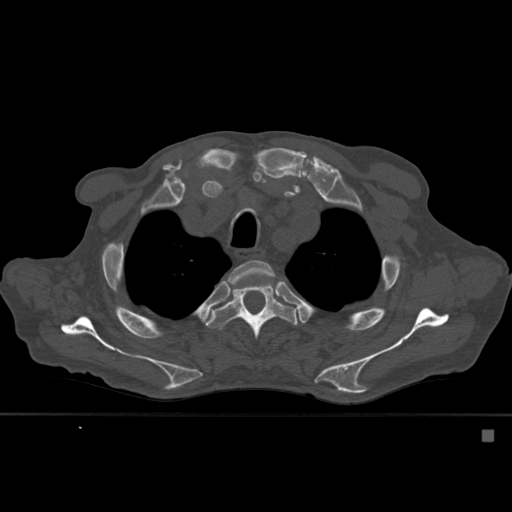
CT including the spine, one axial slice. Slice 421 of 527 in the series (ordered by position). Bone window (W 1800 / L 400 HU). 512 × 512 image matrix, field of view 373 × 373 mm. Patient: male, 78 years. Case-level facts recorded for this patient, not image findings: primary cancer: prostate.
Outlined on this slice (semi-automatic segmentation, software-assisted and operator-edited):
- T3 vertebra: box from (x=228, y=260) to (x=277, y=289) px
- T4 vertebra: (x=205, y=278)–(x=298, y=341)